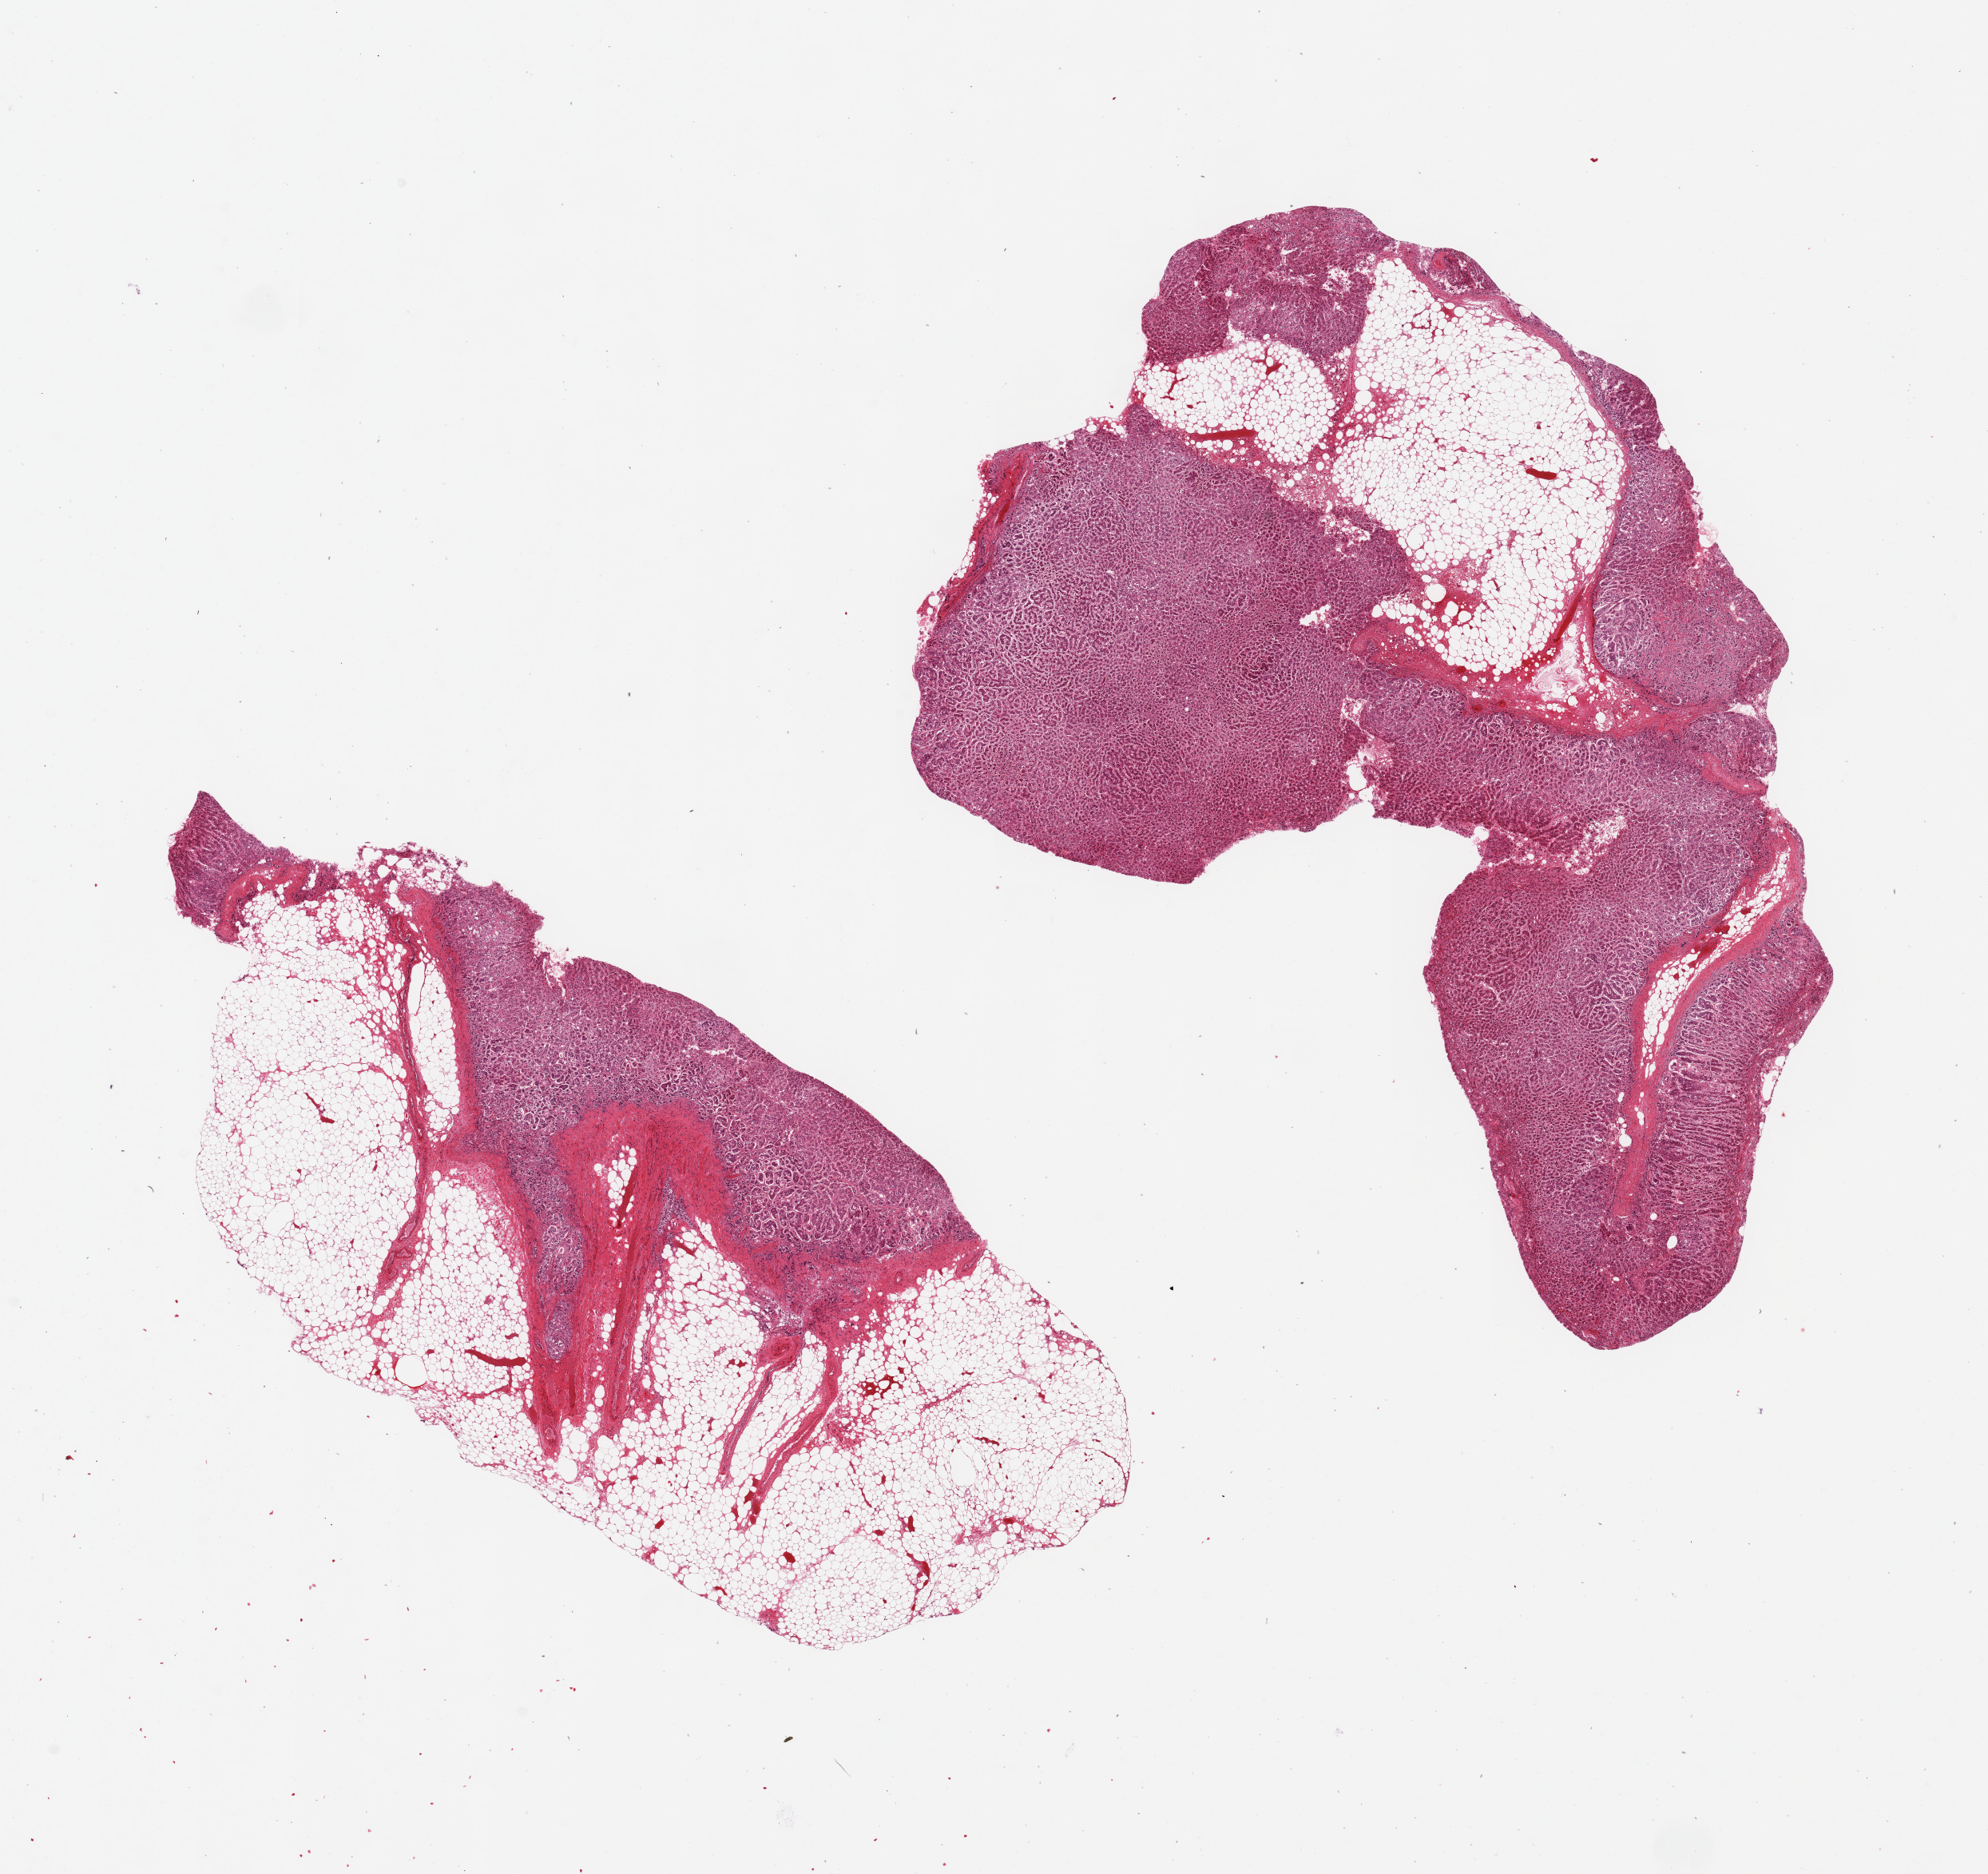
Whole-slide image, H&E stain, brightfield, whole scanned area (about 19.7 x 18.6 mm, acquisition: 20x scan) shown as a low-resolution overview. PAXgene-fixed paraffin-embedded (PFPE) section. Target tissue: adrenal gland. Donor tissue sample. Male donor.
* reviewer comment on this tissue sample: 2 pieces ~9x2mm. Adherent/interstitial fat is ~40% of specimens ~3-4mm wide